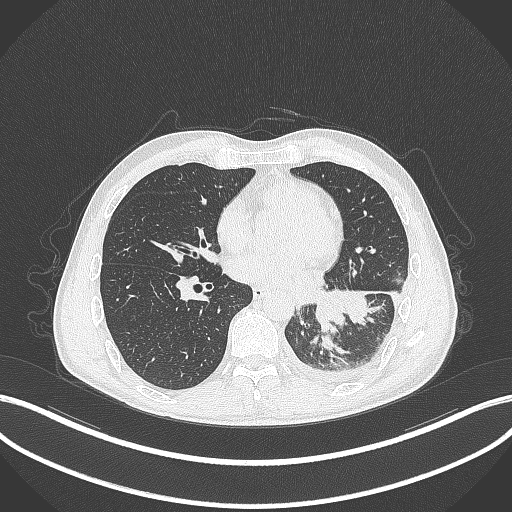
Chest CT, one axial slice. Slice 132 of 295 in the series (ordered by position). Reconstruction kernel B70f. Lung window (W 1500 / L -600 HU). 512 × 512 image matrix, field of view 400 × 400 mm. Male patient, age 47 years. From the clinical record (not read from this slice): clinical TNM (as recorded): T3 N1 M1c.
Outlined on this slice (rectangle marked by the reading radiologist):
- lung tumour (recorded histology: small cell carcinoma): box from (x=311, y=287) to (x=346, y=333) px